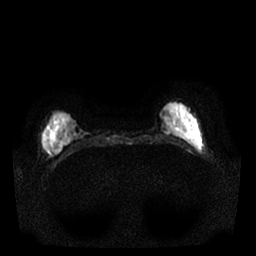
Breast MRI, one axial slice. Position 4 of 25 along the scan axis. Diffusion-weighted series; image 2 of 4 stored at this slice position (different b-values; order by instance number). 1.5 T. 4 mm slice thickness. 256 × 256 image matrix, field of view 340 × 340 mm. Female patient.
Structures marked on this image (expert manual segmentation):
- tumour on diffusion-weighted imaging: bounding box <45,144,50,152> (left, top, right, bottom; pixels)